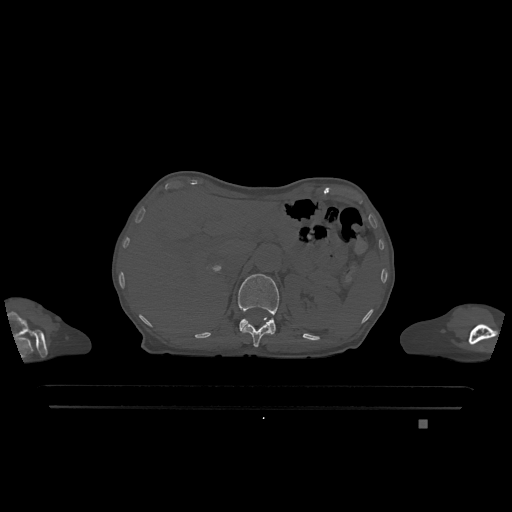
CT including the spine, one axial slice; bone window (W 1800 / L 400 HU); 512 × 512 image matrix. Patient: female, 74 years. From the clinical record (not read from this slice): primary cancer: lung; vertebrae with lytic lesions (as recorded): T1, T4, T5, T6, L4, L5.
Outlined on this slice (semi-automatically segmented with operator editing):
- L1 vertebra: bounding box <238,274,279,335> (left, top, right, bottom; pixels)
- T12 vertebra: <241,318,271,347>